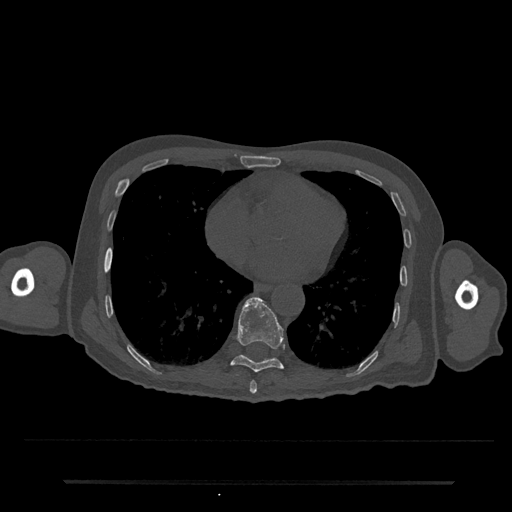
CT including the spine, one axial slice; position 363 of 797 along the scan axis; bone window (W 1800 / L 400 HU); 512 × 512 image matrix, field of view 427 × 427 mm. Male patient, age 74 years. Case-level facts recorded for this patient, not image findings: primary cancer: prostate.
Outlined on this slice (semi-automatically segmented with operator editing):
- T8 vertebra: box from (x=250, y=381) to (x=257, y=394) px
- T9 vertebra: (x=230, y=296)–(x=284, y=373)